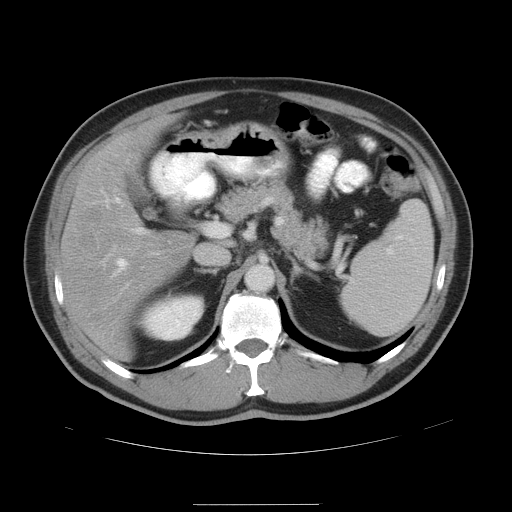
Contrast-enhanced abdominal CT, one axial slice; position 28 of 47 along the scan axis; 120 kVp; intravenous contrast given; soft-tissue window (W 400 / L 40 HU); 5 mm slice thickness; 512 × 512 image matrix, field of view 420 × 420 mm. Male patient, age 61 years. From the clinical record (not read from this slice): diagnosis: colorectal cancer liver metastases, imaged before liver resection; multiple liver metastases: no; largest metastasis: 1.2 cm; disease in both lobes: no.
Structures marked on this image (outlined manually by an expert reader):
- hepatic veins: box from (x=115, y=197) to (x=127, y=274) px
- liver: (x=62, y=120)–(x=194, y=362)
- planned liver remnant (the part of the liver to remain after resection): (x=64, y=121)–(x=194, y=362)
- portal vein (with intrahepatic branches): (x=135, y=222)–(x=218, y=233)